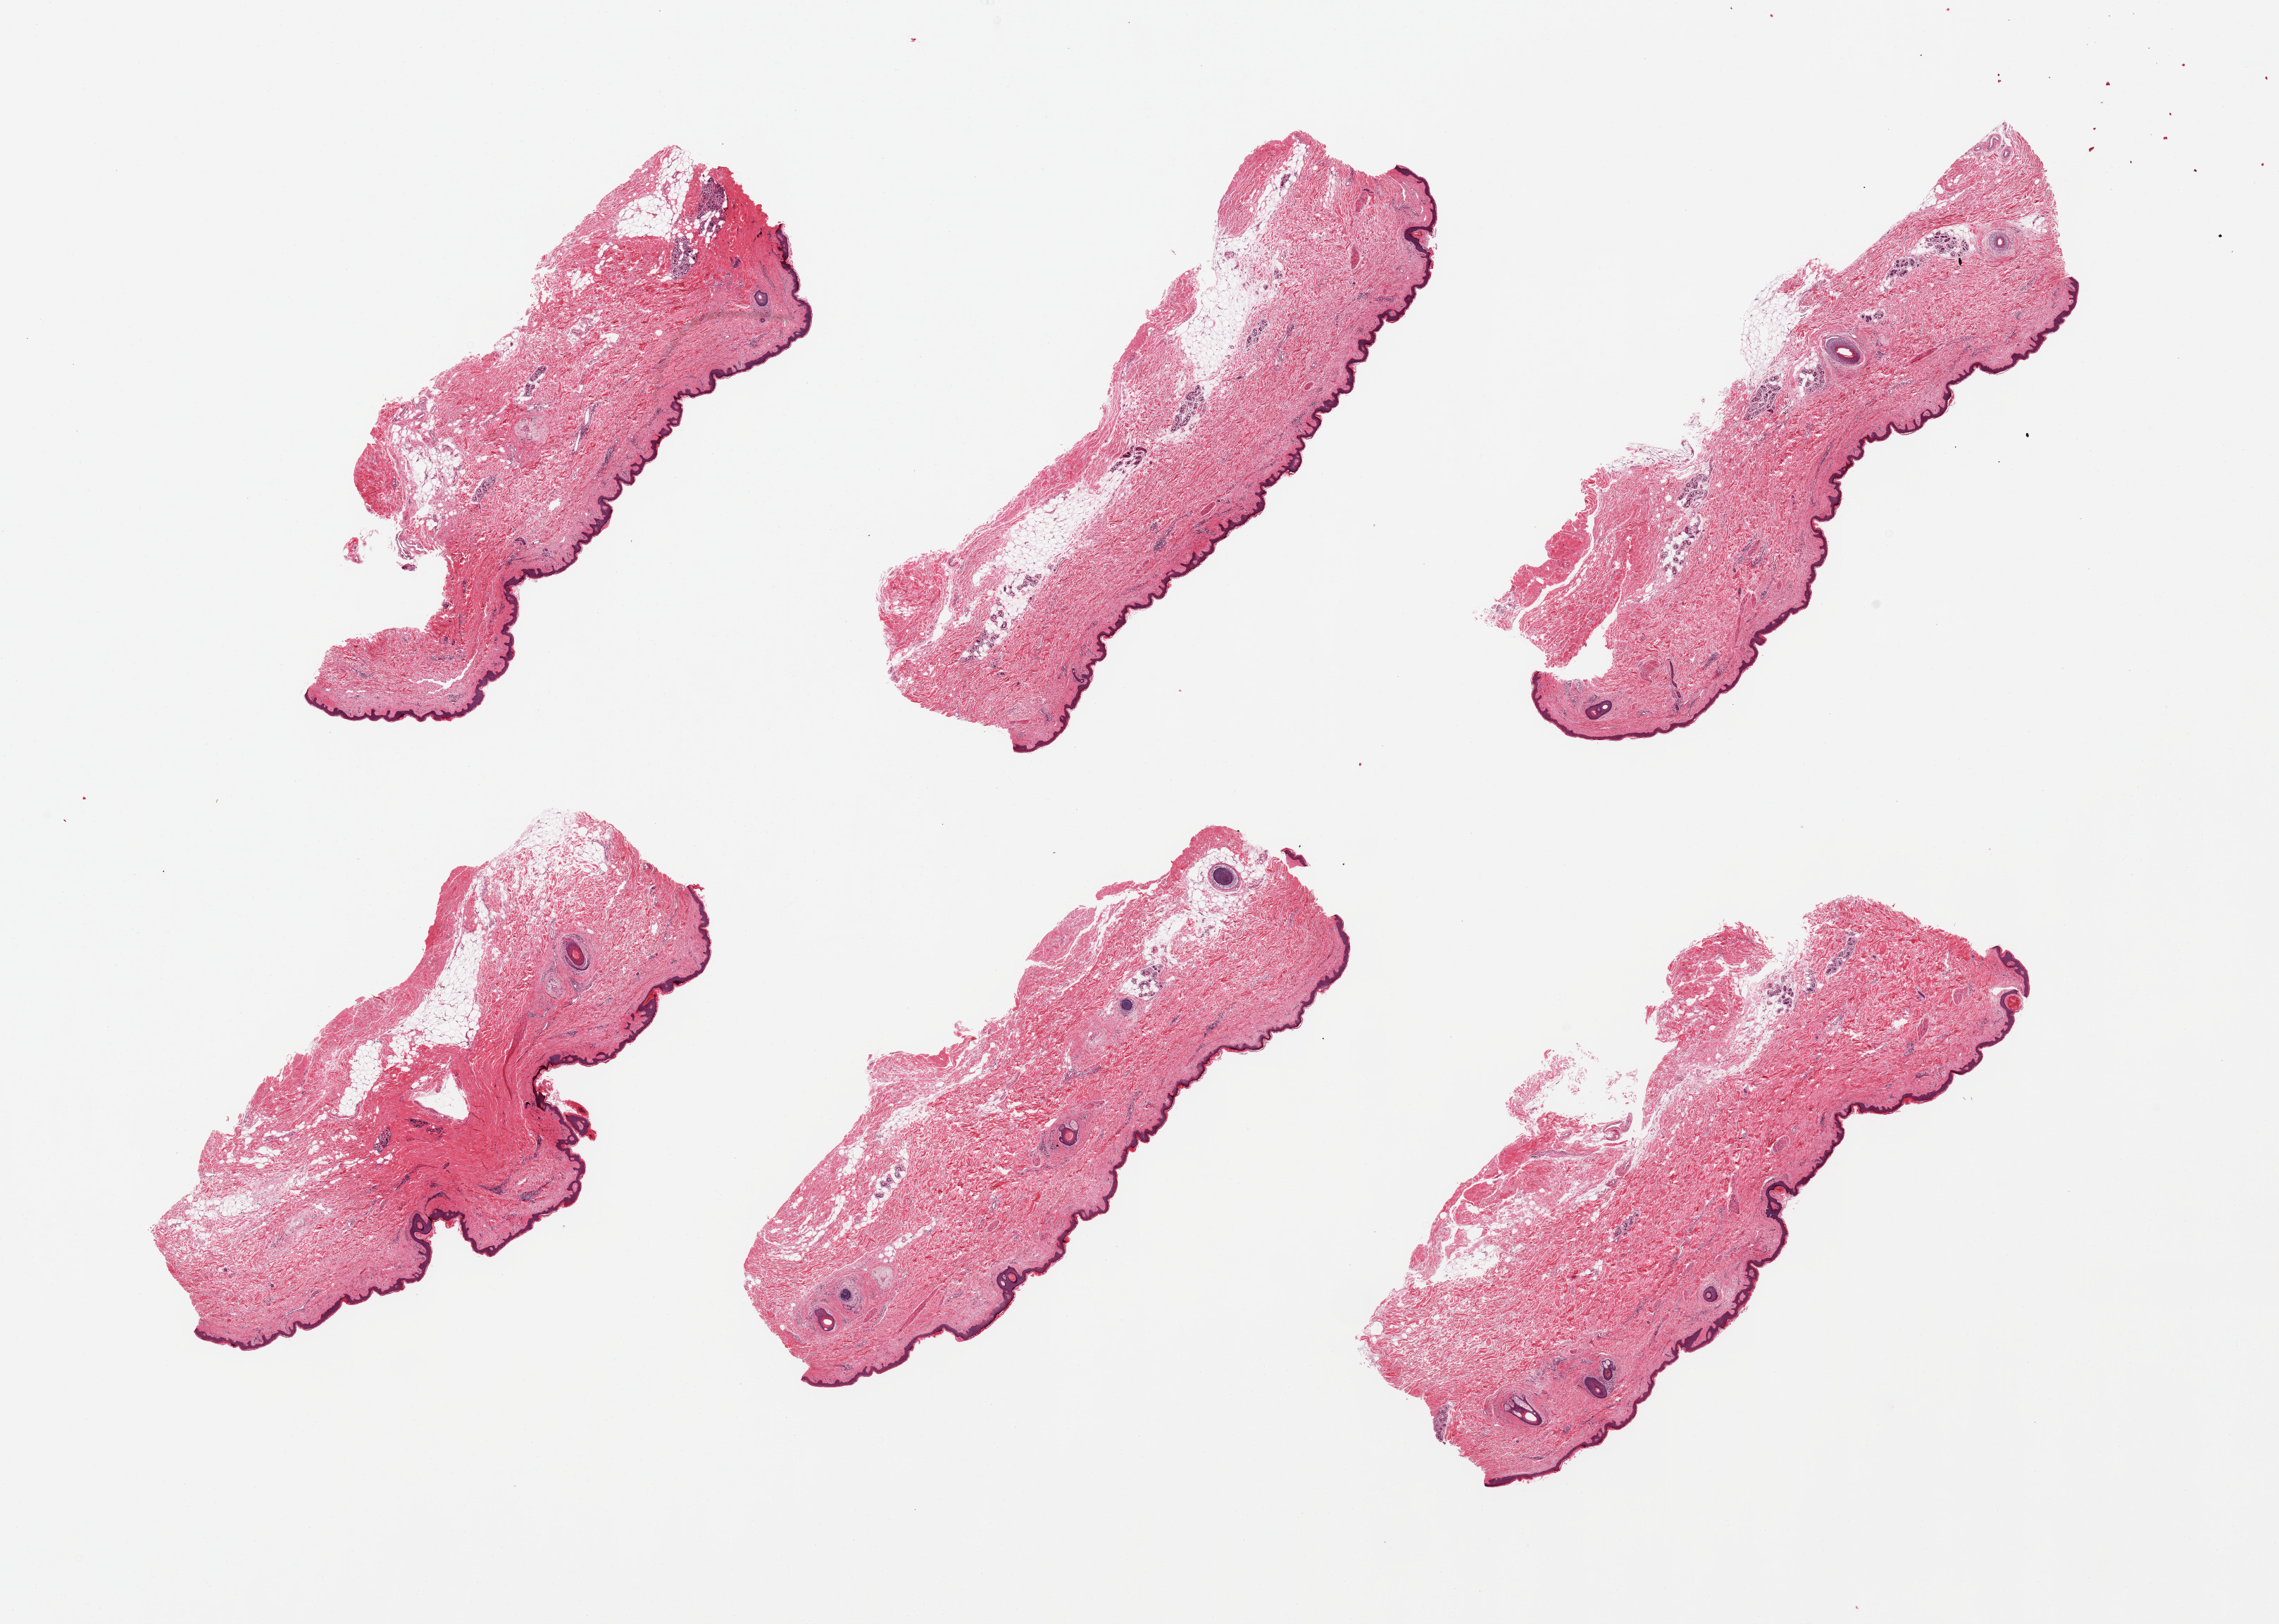
Digitized H&E-stained section, brightfield, low-resolution overview of the scanned area, about 25.6 x 18.2 mm, PAXgene-fixed paraffin-embedded (PFPE) section, section of skin of suprapubic region (target tissue), donor tissue sample. Male donor.
Pathologist's review note for this sample: 6 pieces; well trimmed; 10-20% dermal fat.